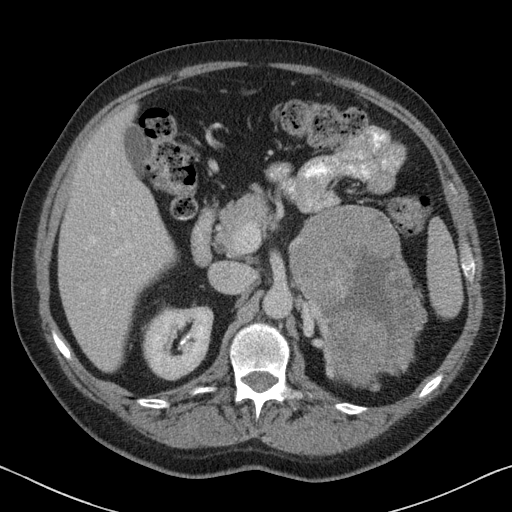
Contrast-enhanced abdominal CT, one axial slice; position 46 of 88 along the scan axis; reconstruction kernel B31f; 120 kVp; soft-tissue window (W 400 / L 40 HU); 3 mm slice thickness; 512 × 512 image matrix, field of view 366 × 366 mm. Patient: male, 51 years. From the clinical record (not read from this slice): diagnosis: adrenocortical carcinoma; tumour side: left adrenal; tumour size at pathology: 16.5 cm; Ki-67 index: 30 %; stage (as recorded): 2.
Structures marked on this image (semi-automatic segmentation, software-assisted and operator-edited):
- mass: box from (x=291, y=206) to (x=425, y=385) px